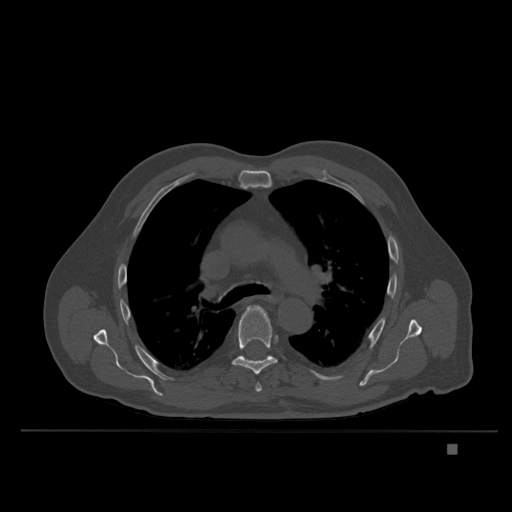
CT including the spine, one axial slice. Slice 260 of 435 in the series (ordered by position). Bone window (W 1800 / L 400 HU). 1.5 mm slice thickness. 512 × 512 image matrix, field of view 434 × 434 mm. Male patient, age 73 years. Case-level facts recorded for this patient, not image findings: primary cancer: skin.
Structures marked on this image (semi-automatic segmentation, software-assisted and operator-edited):
- T5 vertebra: bounding box [x1, y1, x2, y2] px = [255, 383, 262, 392]
- T6 vertebra: [232, 305, 277, 375]
- T7 vertebra: [242, 356, 267, 359]